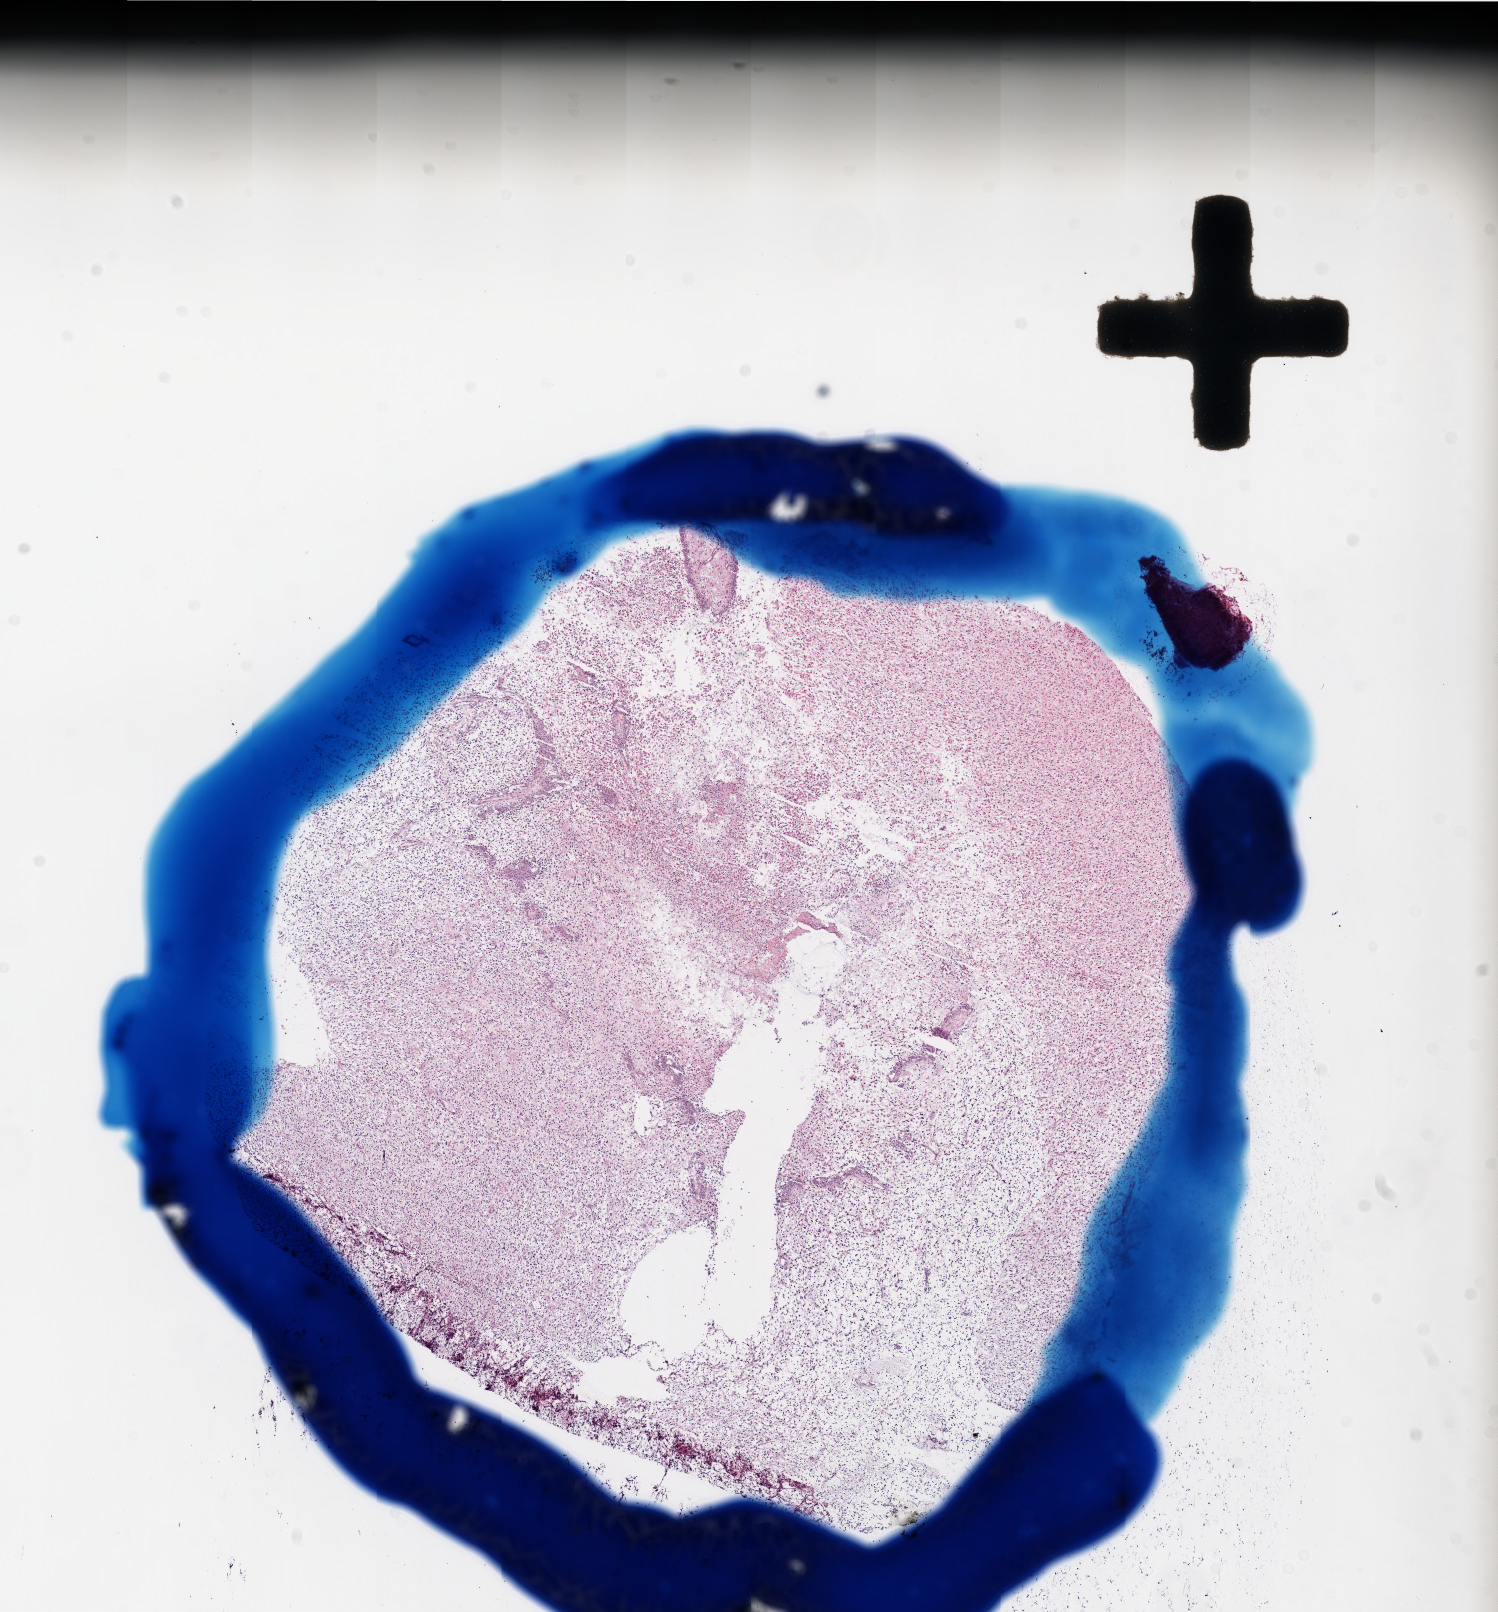
Hematoxylin and eosin (H&E) stained whole-slide image — low-resolution overview of the scanned area, about 12.0 x 12.9 mm (from a 20x scan); frozen section from the top of the tissue portion; primary tumour sample from the brain. Male, age 66 years at initial diagnosis. Slide review estimates, as recorded: tumour cells 95%, tumour nuclei 100%, normal cells 0%, stromal cells 0%, necrosis 5%.
Pathologic diagnosis: Glioblastoma.